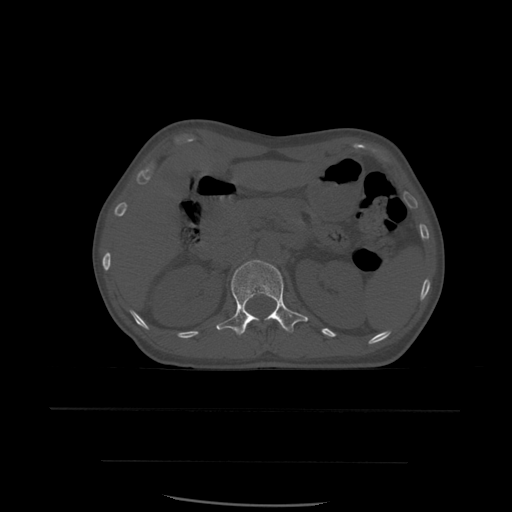
CT including the spine, one axial slice; slice 252 of 574 in the series (ordered by position); bone window (W 1800 / L 400 HU); 1.25 mm slice thickness; 512 × 512 image matrix. Patient age 48 years. Case-level facts recorded for this patient, not image findings: primary cancer: lung.
Annotated regions visible in this slice (semi-automatically segmented with operator editing):
- L1 vertebra: bounding box <216,260,309,336> (left, top, right, bottom; pixels)